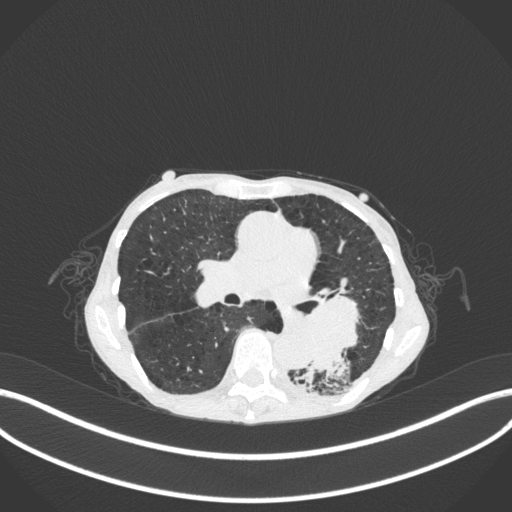
Chest CT, one axial slice. Slice 148 of 347 in the series (ordered by position). Reconstruction kernel B31f. 120 kVp. Lung window (W 1500 / L -600 HU). 1 mm slice thickness. 512 × 512 image matrix, field of view 400 × 400 mm. Patient: female, 70 years. Case-level facts recorded for this patient, not image findings: clinical TNM (as recorded): T3 N0 M0.
Structures marked on this image (rectangle marked by the reading radiologist):
- lung tumour (recorded histology: small cell carcinoma): bounding box [x1, y1, x2, y2] px = [283, 288, 369, 378]